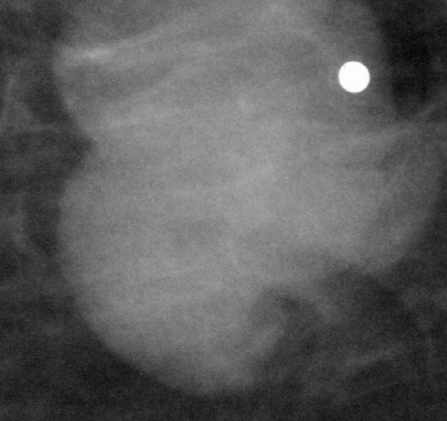
Crop from a digitized film mammogram around one marked abnormality, left breast, CC view, BI-RADS breast density category 1 (scale 1–4).
Finding: mass, shape lobulated, margins circumscribed; BI-RADS assessment category 5; subtlety rating 5 on a 1 (subtle) to 5 (obvious) scale; pathology result (as recorded, not read from the image): malignant.